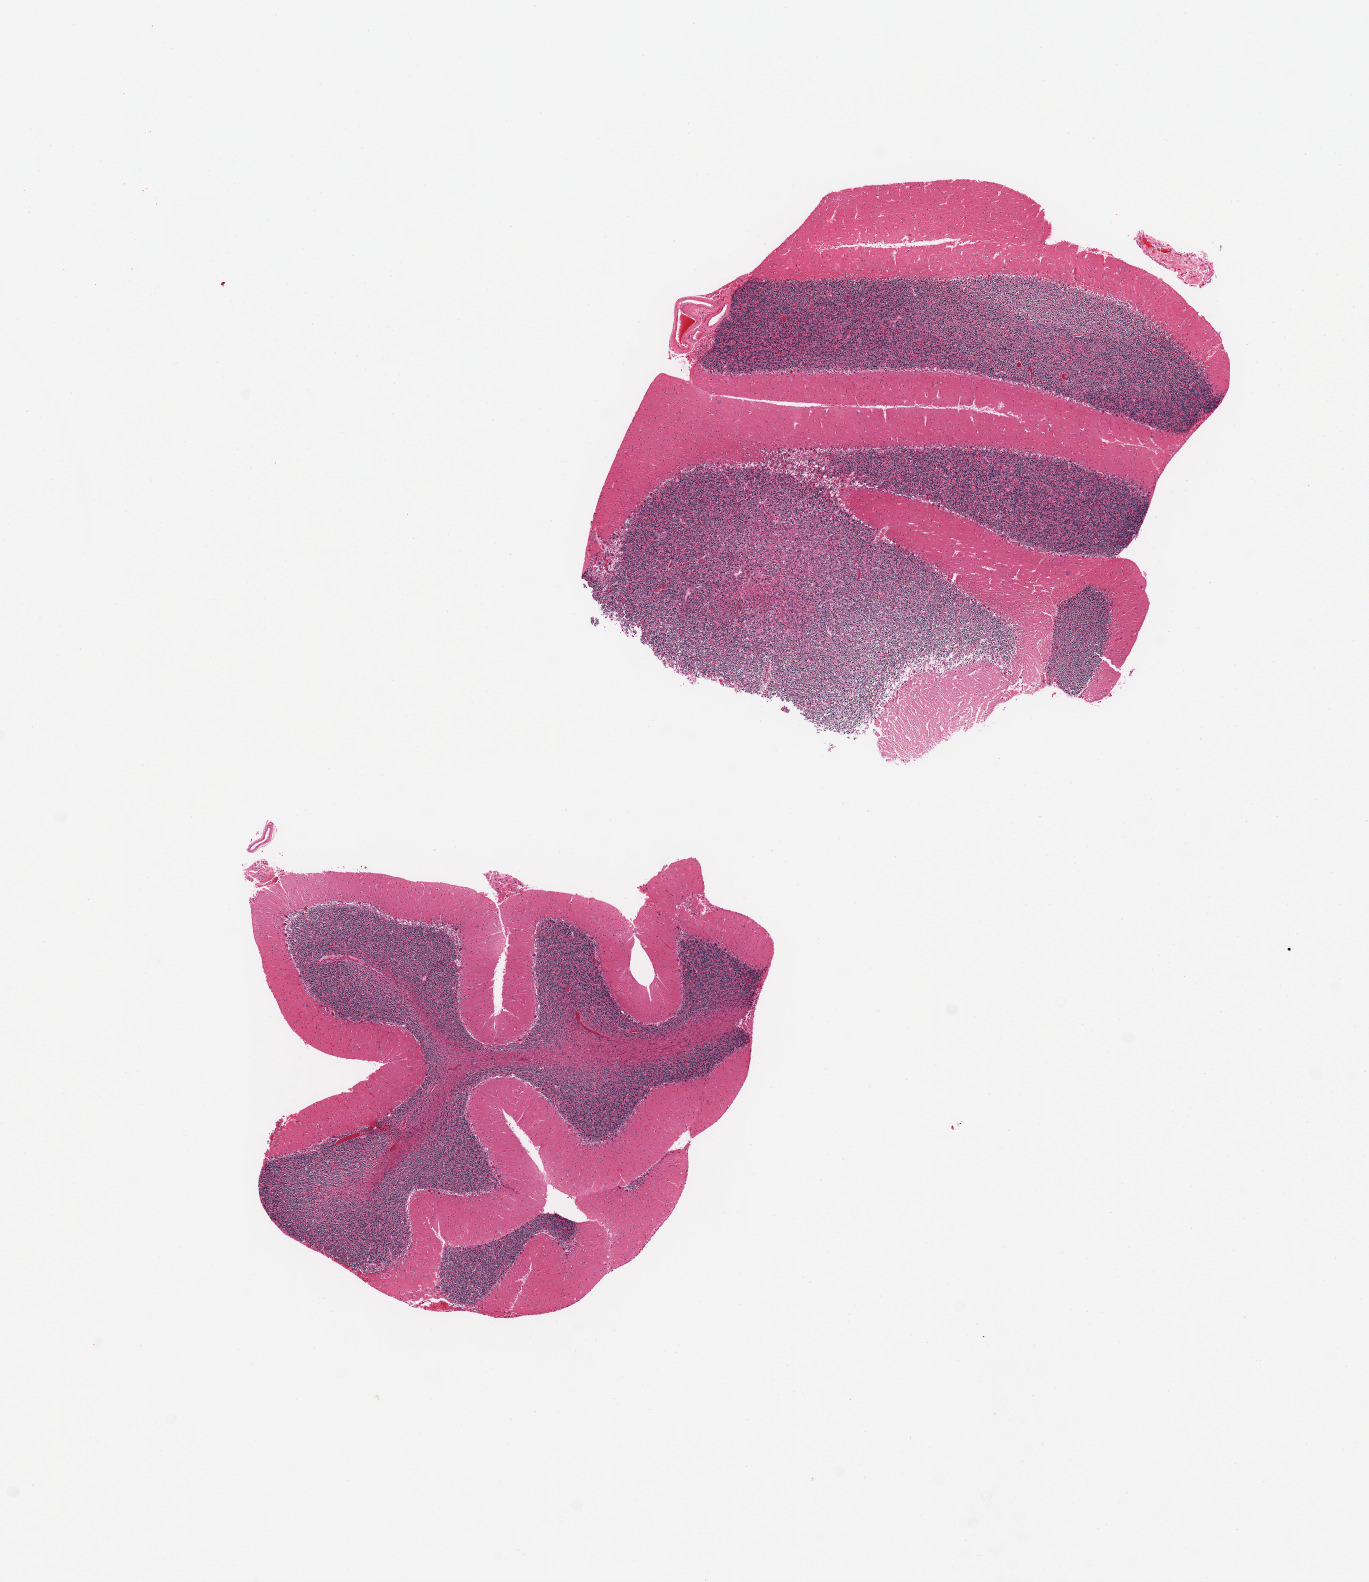
Digitized haematoxylin and eosin-stained section, low-resolution overview of the scanned area, about 10.8 x 12.5 mm. PAXgene-fixed paraffin-embedded (PFPE) section. Target tissue: cerebellum. Tissue donor sample.
Review note (as recorded): 2 pieces 4.2 mm.